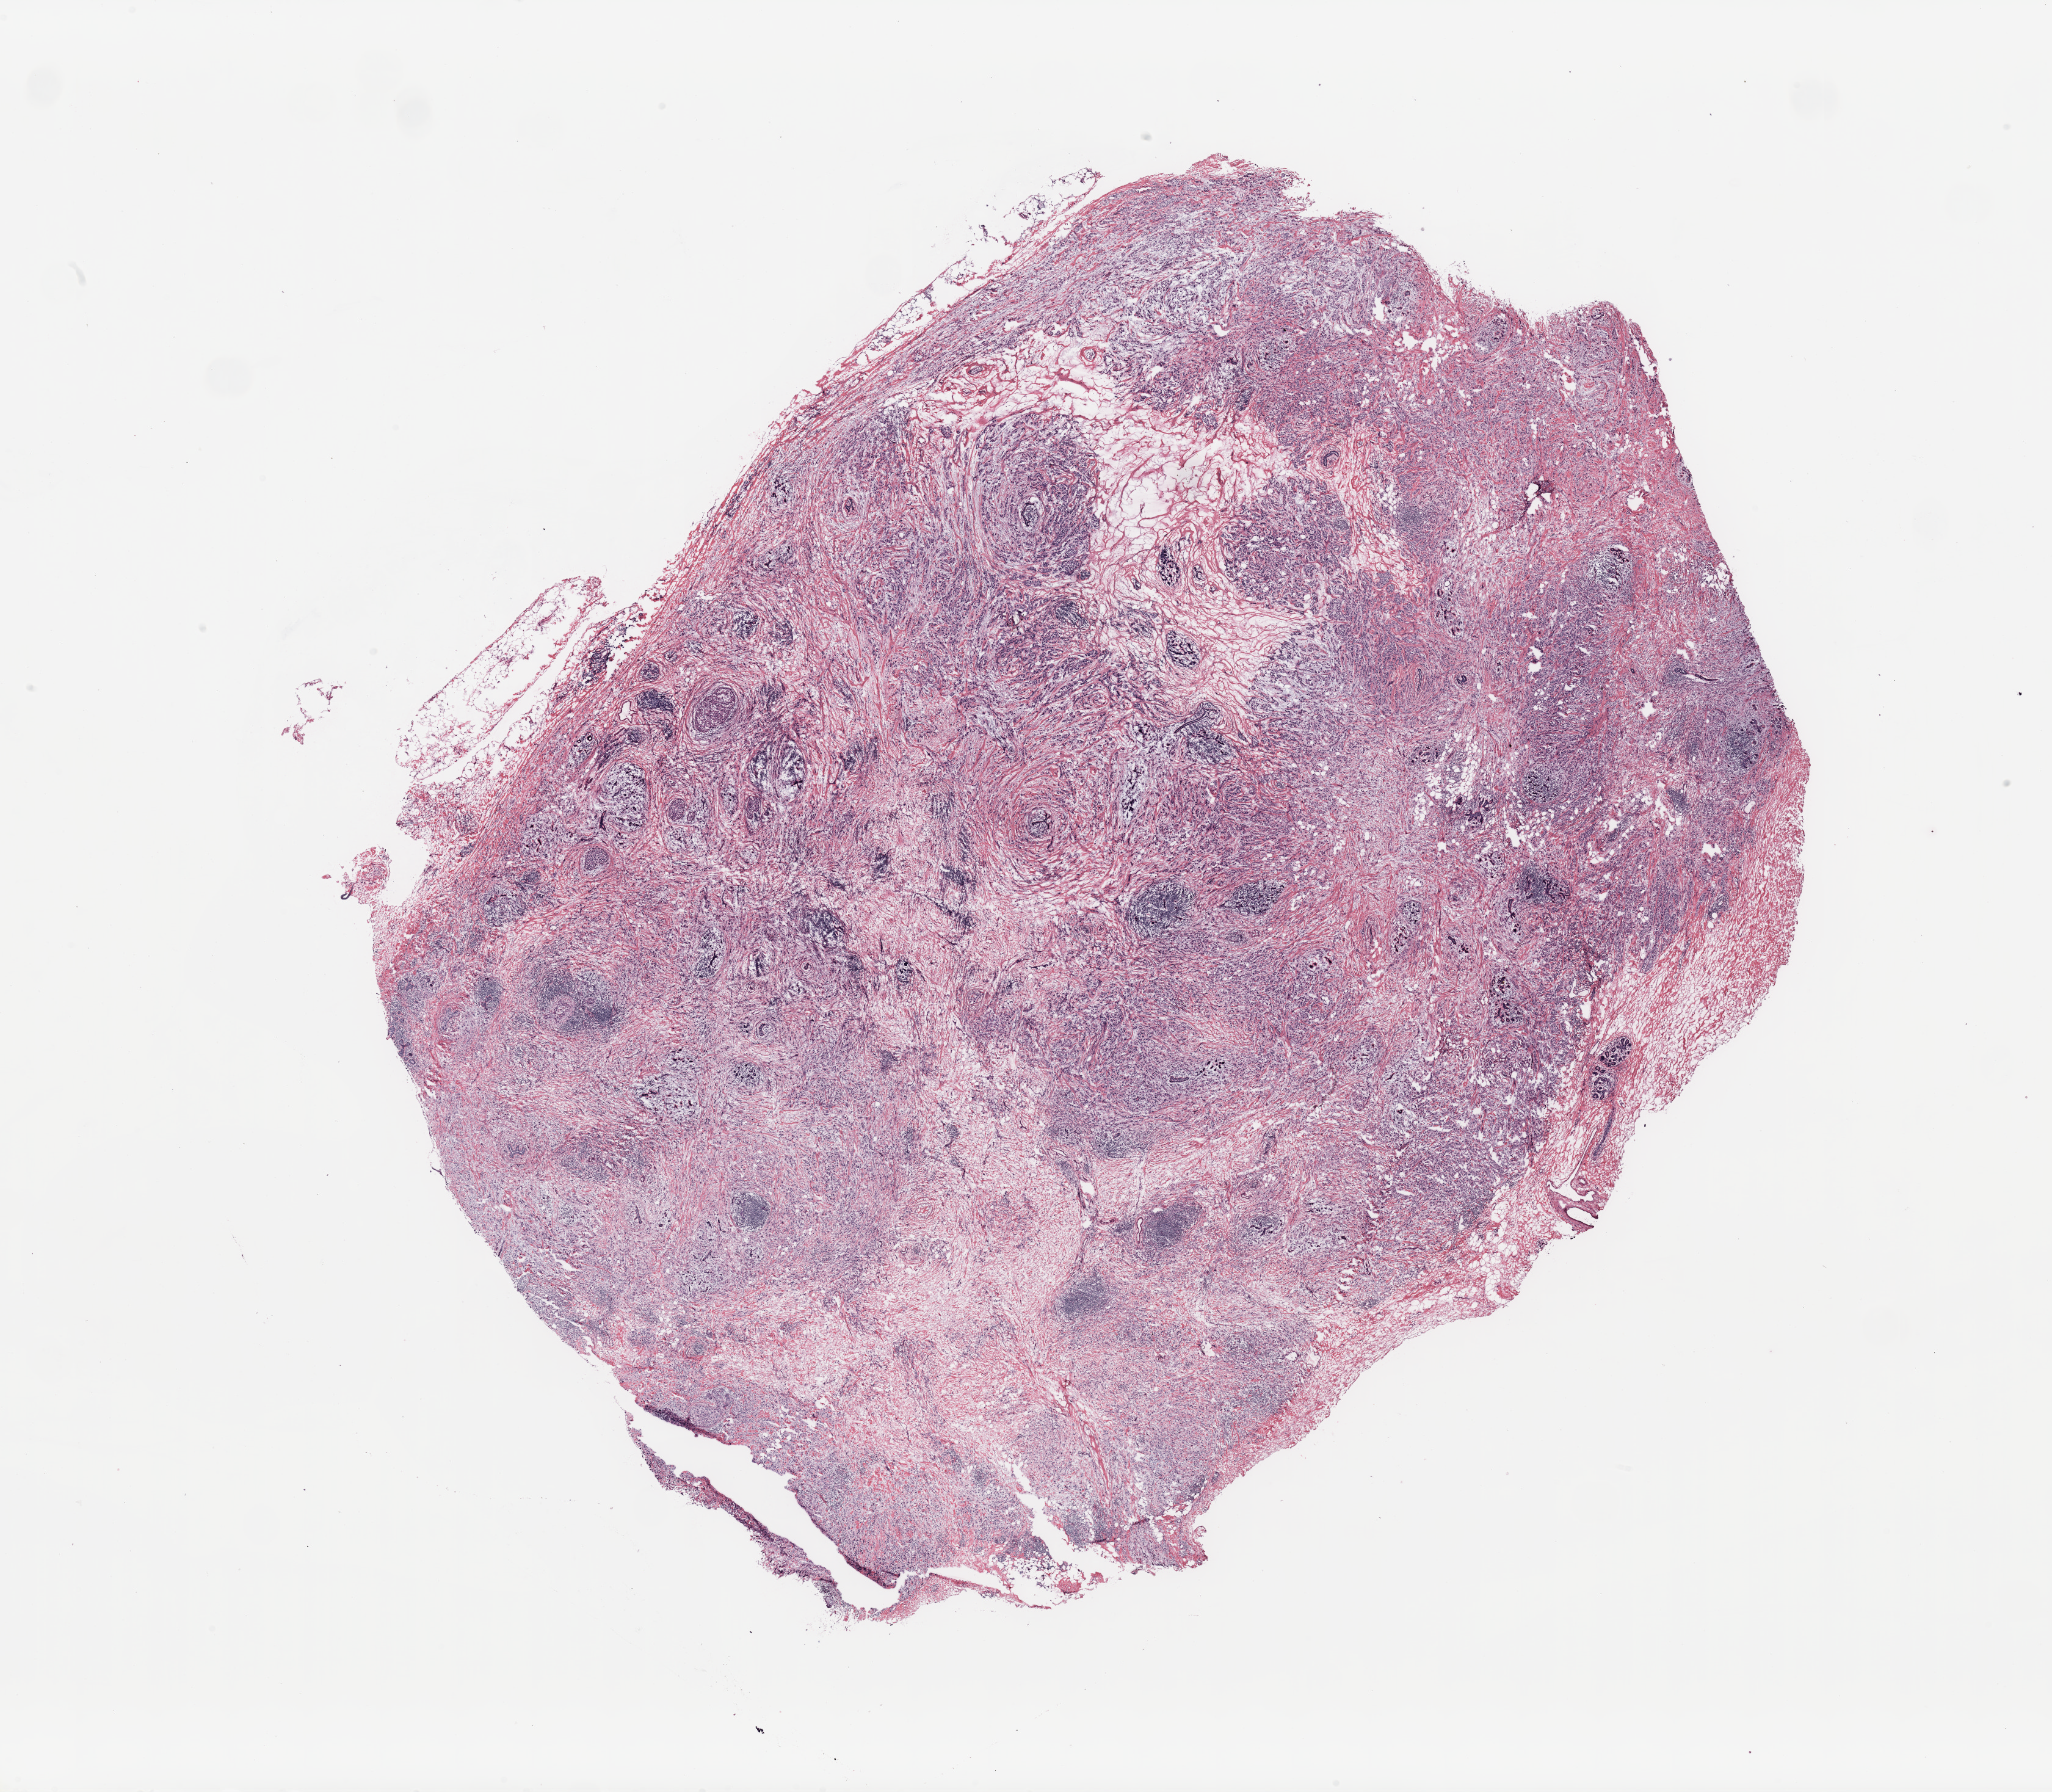
H&E-stained whole-slide image, a low-resolution overview of the entire scanned area, about 26.6 x 23.2 mm (slide scanned at 20x). Breast, tissue type not recorded.
Patient diagnosis (cohort enrolment): breast cancer (breast).